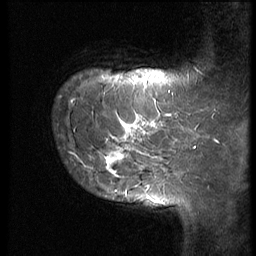
Breast MRI (dynamic contrast-enhanced), one sagittal slice; position 8 of 62 along the scan axis; 3 images stored at this slice position (order not interpretable as contrast timing); 1.5 T; TE 4.2 ms, TR 9 ms; 256 × 256 image matrix, field of view 180 × 180 mm. Female patient, age 28 years. From the clinical record (not read from this slice): setting: breast cancer imaged before/during neoadjuvant chemotherapy.
Outlined on this slice (semi-automatically segmented with operator editing):
- analysis volume of interest (the breast-tissue region the enhancement analysis was run in; not a lesion): box from (x=52, y=84) to (x=192, y=180) px
- tumour enhancement mask (voxels above the 140 % enhancement threshold inside the analysis volume of interest): (x=106, y=114)–(x=192, y=176)